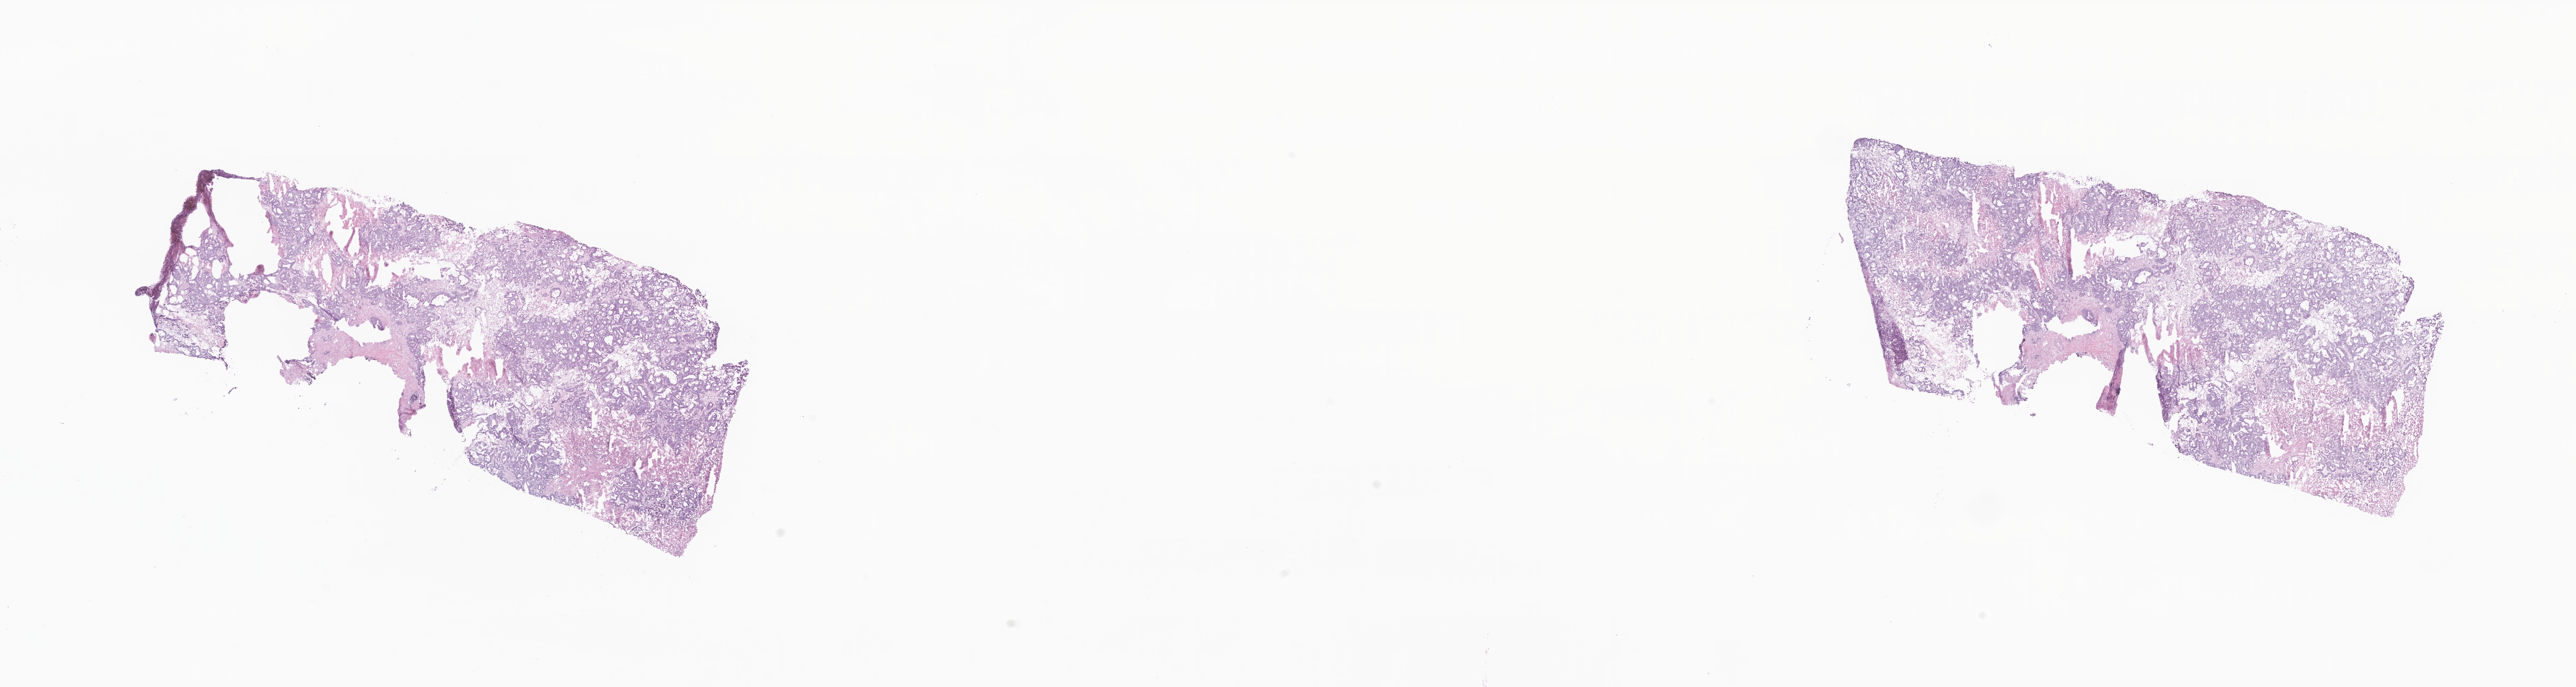
Digitized haematoxylin and eosin-stained section, whole scanned area (about 35.9 x 9.6 mm) shown as a low-resolution overview; frozen section (tissue freezing medium); specimen: metastatic tumor tissue, resected from liver. Patient: female, age at initial diagnosis 49 years. Composition of this section per pathologist review: tumor cells 60%, tumor nuclei 87%, stromal cells 17%, necrosis 14%, normal cells 9%. Infiltration values recorded for this section: lymphocyte infiltration 1%, monocyte infiltration 1%, neutrophil infiltration 0%.
Section: bottom of the tissue portion. Patient diagnosis (primary): Adenocarcinoma, NOS.